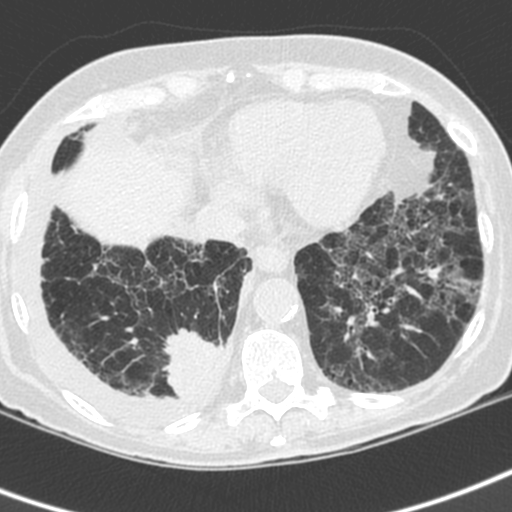
Chest CT (low-dose screening protocol), one axial image; baseline annual screen; lung window (W 1500 / L -600 HU); 1.3 mm slice thickness; 120 kVp; slice 144 of 192 in the series. Female participant, aged 73 years at enrolment. Current smoker at enrolment.
- Expert-annotated lung lesion, bounding box (x1, y1, x2, y2) in pixels: (157, 321, 234, 406).
- The exam's reader record, not a measurement of the box and not confirmed to be the same lesion: non-calcified nodule or mass ≥4 mm, right lower lobe, 35 × 30 mm, spiculated (stellate) margins, soft tissue attenuation.
- Participant outcome: lung cancer diagnosed 22 days after this screen — adenocarcinoma, NOS, right lower lobe, stage IV (AJCC 6th edition), 35 mm at pathology.